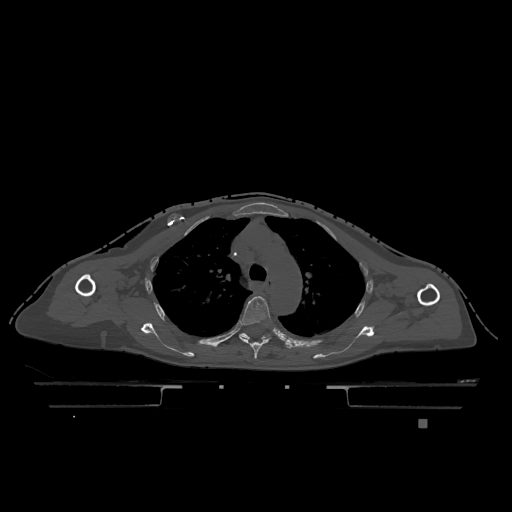
CT including the spine, one axial slice; position 868 of 1317 along the scan axis; bone window (W 1800 / L 400 HU); 512 × 512 image matrix, field of view 500 × 500 mm. Female patient, age 74 years. Case-level facts recorded for this patient, not image findings: primary cancer: lung.
Annotated regions visible in this slice (semi-automatic segmentation, software-assisted and operator-edited):
- T4 vertebra: bounding box [x1, y1, x2, y2] px = [239, 296, 271, 359]
- T5 vertebra: [239, 333, 269, 339]